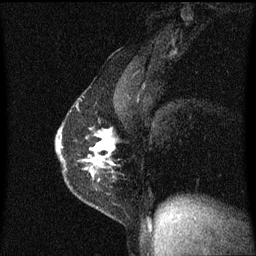
Breast MRI (dynamic contrast-enhanced), one sagittal slice. Dynamic contrast-enhanced series, image 2 of 3 at this slice position (ordered by acquisition). 1.5 T. TE 4.2 ms, TR 8.4 ms. 256 × 256 image matrix, field of view 200 × 200 mm. Female patient, age 40 years.
Structures marked on this image (semi-automatically segmented with operator editing):
- analysis volume of interest (the breast-tissue region the enhancement analysis was run in; not a lesion): bounding box [x1, y1, x2, y2] px = [57, 110, 118, 191]
- tumour enhancement mask (voxels above the 70 % enhancement threshold inside the analysis volume of interest): [57, 130, 115, 181]